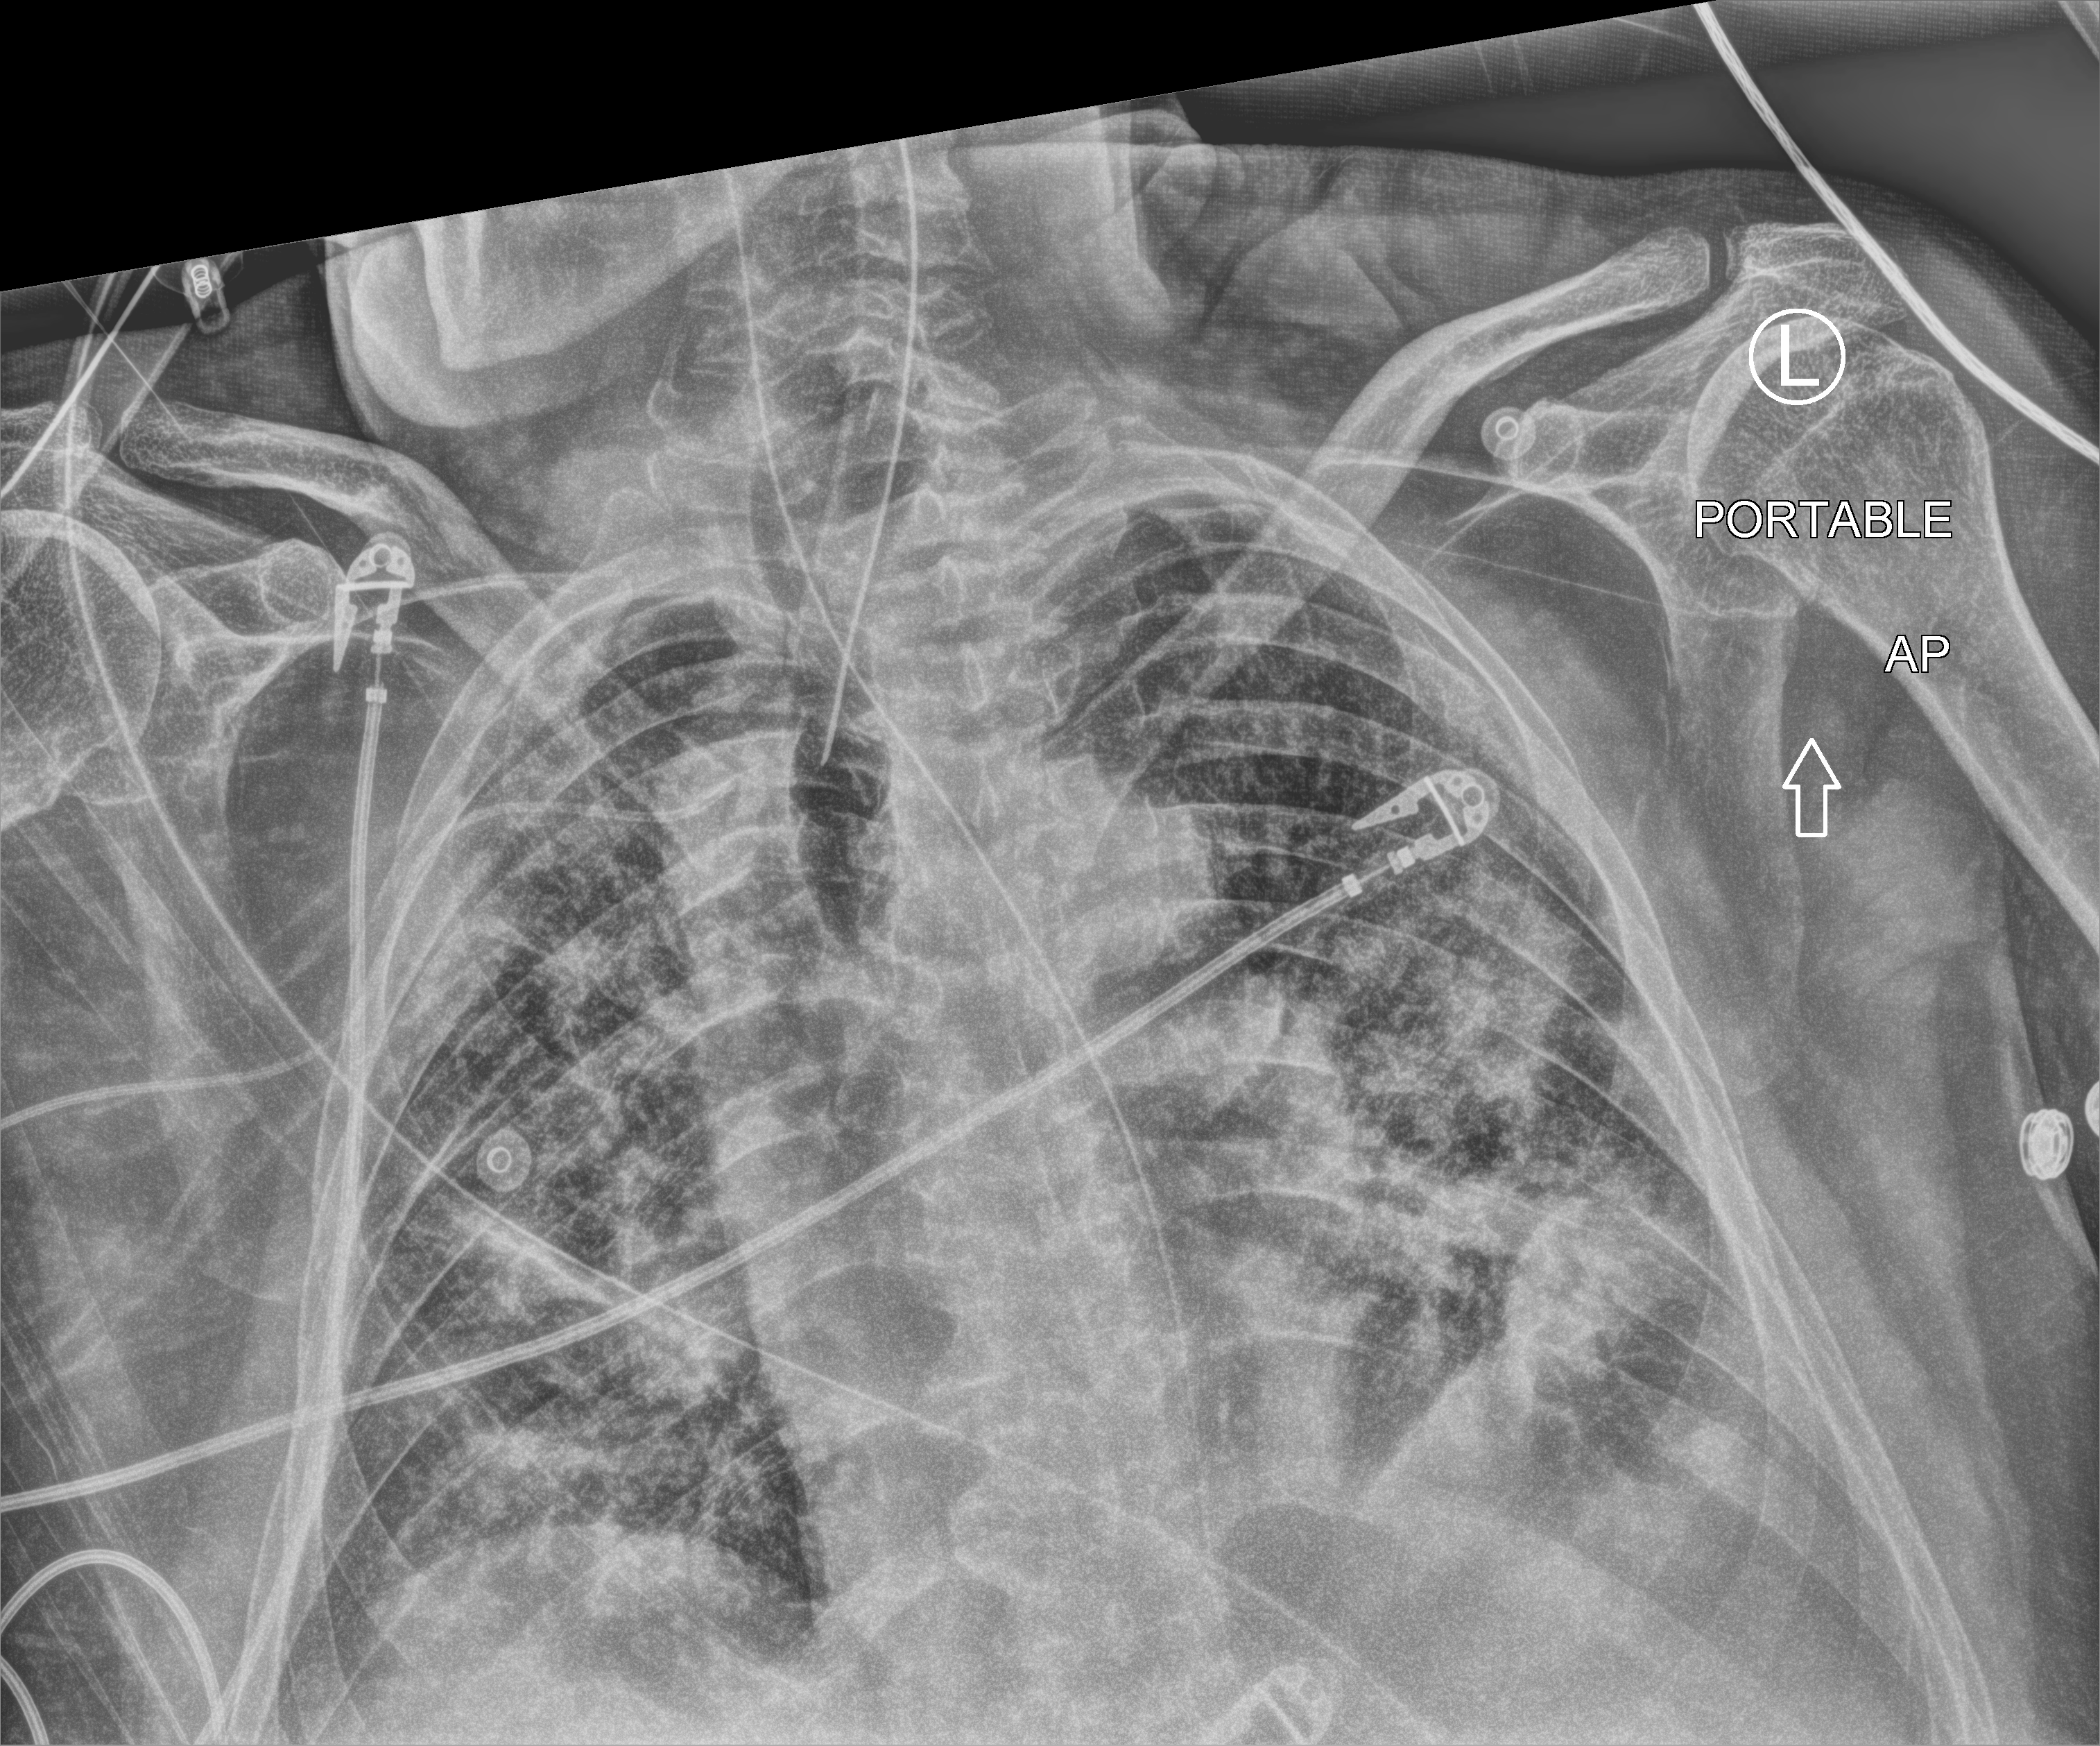
Portable chest radiograph, anteroposterior (AP) projection. Male patient hospitalised with COVID-19, age 60–74 years.
Admission-level facts for this patient (not findings on this image; timing relative to this image not recorded):
- length of hospital stay: 24 days
- mechanically ventilated during this hospital stay: yes
- admitted to intensive care during this hospital stay: yes